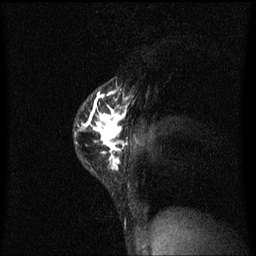
Breast MRI (dynamic contrast-enhanced), one sagittal slice; slice 46 of 60 in the series (ordered by position); dynamic contrast-enhanced series, image 2 of 3 at this slice position (ordered by acquisition); 1.5 T; TE 4.2 ms, TR 8.4 ms; 2 mm slice thickness; 256 × 256 image matrix, field of view 200 × 200 mm. Female patient, age 40 years.
Outlined on this slice (semi-automatic segmentation, software-assisted and operator-edited):
- analysis volume of interest (the breast-tissue region the enhancement analysis was run in; not a lesion): bounding box <76,78,130,183> (left, top, right, bottom; pixels)
- tumour enhancement mask (voxels above the 70 % enhancement threshold inside the analysis volume of interest): <76,92,130,171>